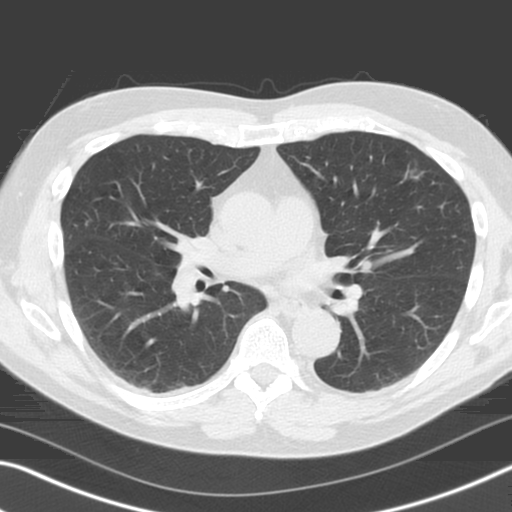
Chest CT (low-dose screening protocol), one axial image; baseline annual screen; lung window (W 1500 / L -600 HU); 3.2 mm slice thickness; slice 83 of 165 in the series; 512 × 512 image matrix. Male, age 71 years at enrolment. Former smoker at enrolment.
Lesion marked by an expert reader, bounding box (x1, y1, x2, y2) in pixels: (397, 154, 439, 191). Screening reader's record for this exam (one nodule recorded; not confirmed to be the boxed lesion): non-calcified nodule or mass ≥4 mm, left upper lobe, 11 × 10 mm, poorly defined margins, ground glass attenuation. Participant outcome: lung cancer diagnosed 289 days after this screen — adenocarcinoma, NOS, left upper lobe, moderately differentiated (G2), stage IA (AJCC 6th edition), 11 mm at pathology.